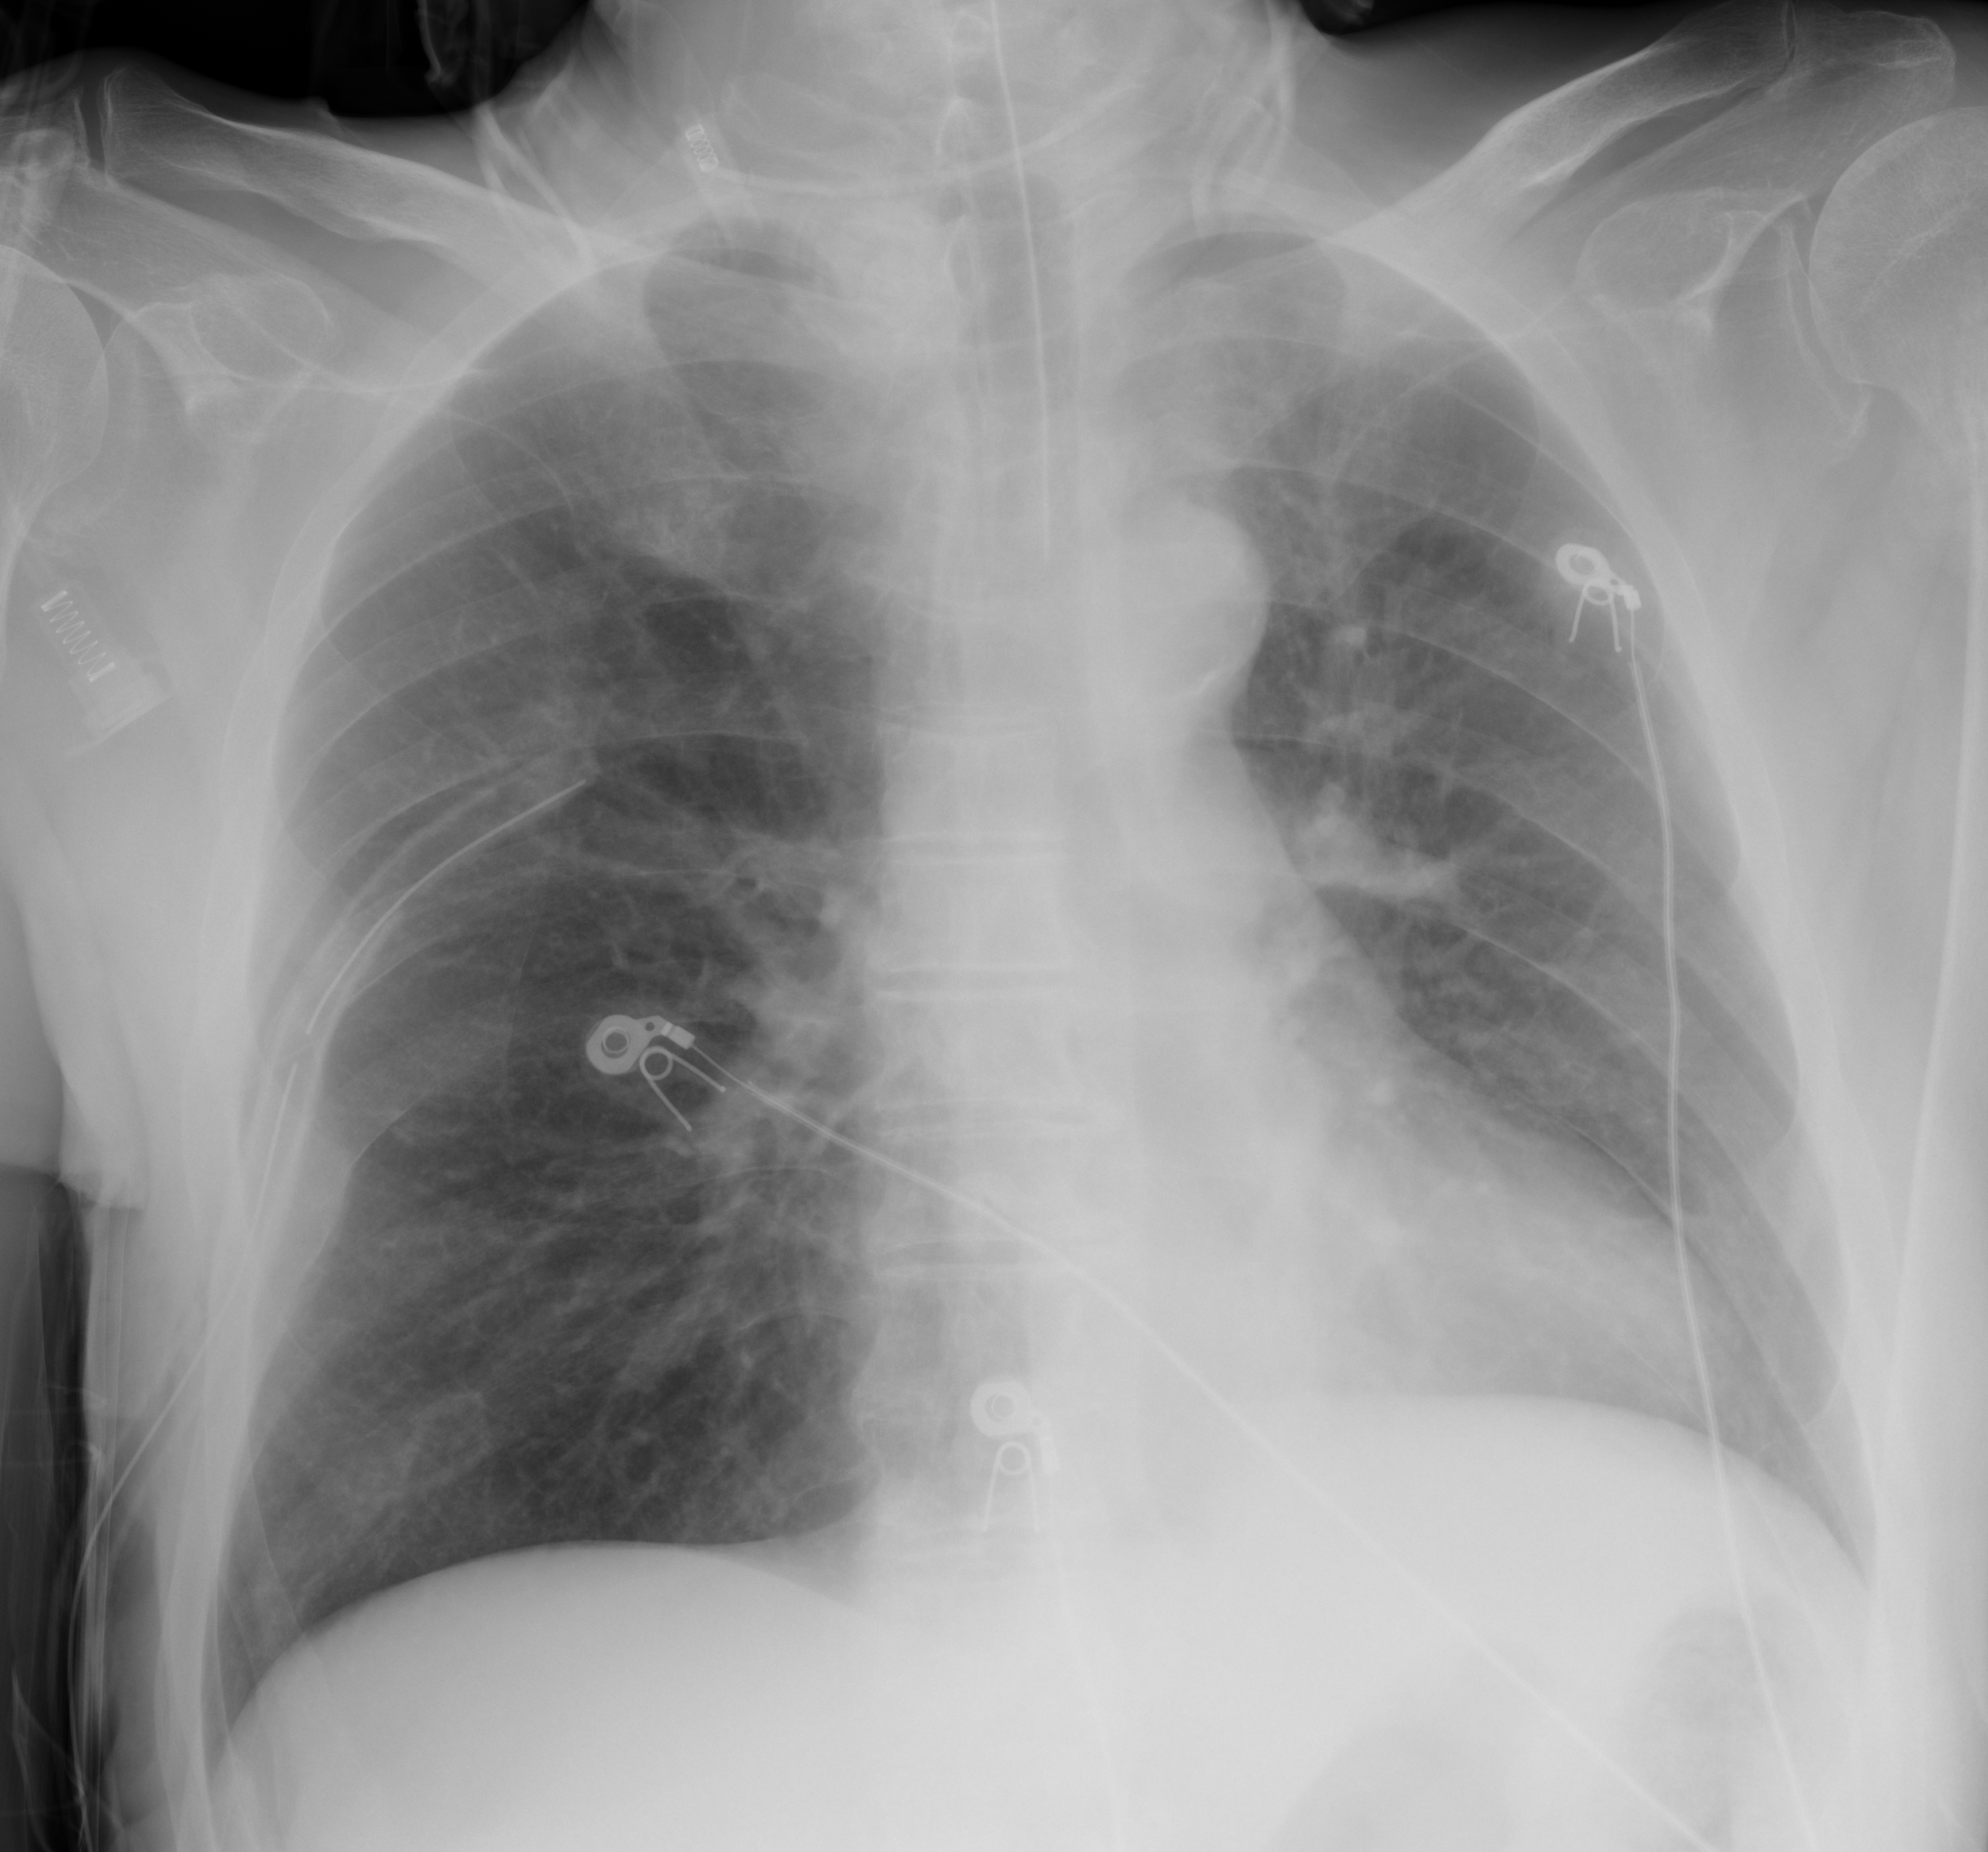
Chest X-ray (portable), AP projection. Male patient, age 59 years; imaged 0 days after the COVID-19 diagnosis.
Radiologist's key findings for this exam: Upper lobe predominant emphysema.